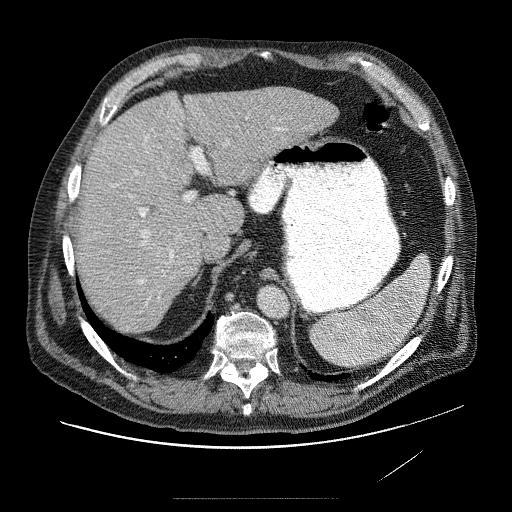
Contrast-enhanced abdominal CT (liver protocol), one axial slice. Reconstruction kernel STANDARD. 120 kVp. Soft-tissue window (W 400 / L 40 HU). 512 × 512 image matrix, field of view 420 × 420 mm. Case-level facts recorded for this patient, not image findings: diagnosis: hepatocellular carcinoma (patient treated with transarterial chemoembolisation; whether this scan precedes or follows treatment is not stated here); TNM stage (as recorded): Stage-IVA; Child-Pugh class: A.
Structures marked on this image (semi-automatically segmented with operator editing):
- abdominal aorta: bounding box (x1, y1, x2, y2) in pixels: (257, 286, 289, 317)
- liver parenchyma outside the tumour (the mass and vessels are separate outlines, so this box may not span the whole liver): (78, 86, 342, 321)
- mass: (143, 97, 198, 184)
- liver vessels: (95, 111, 266, 287)